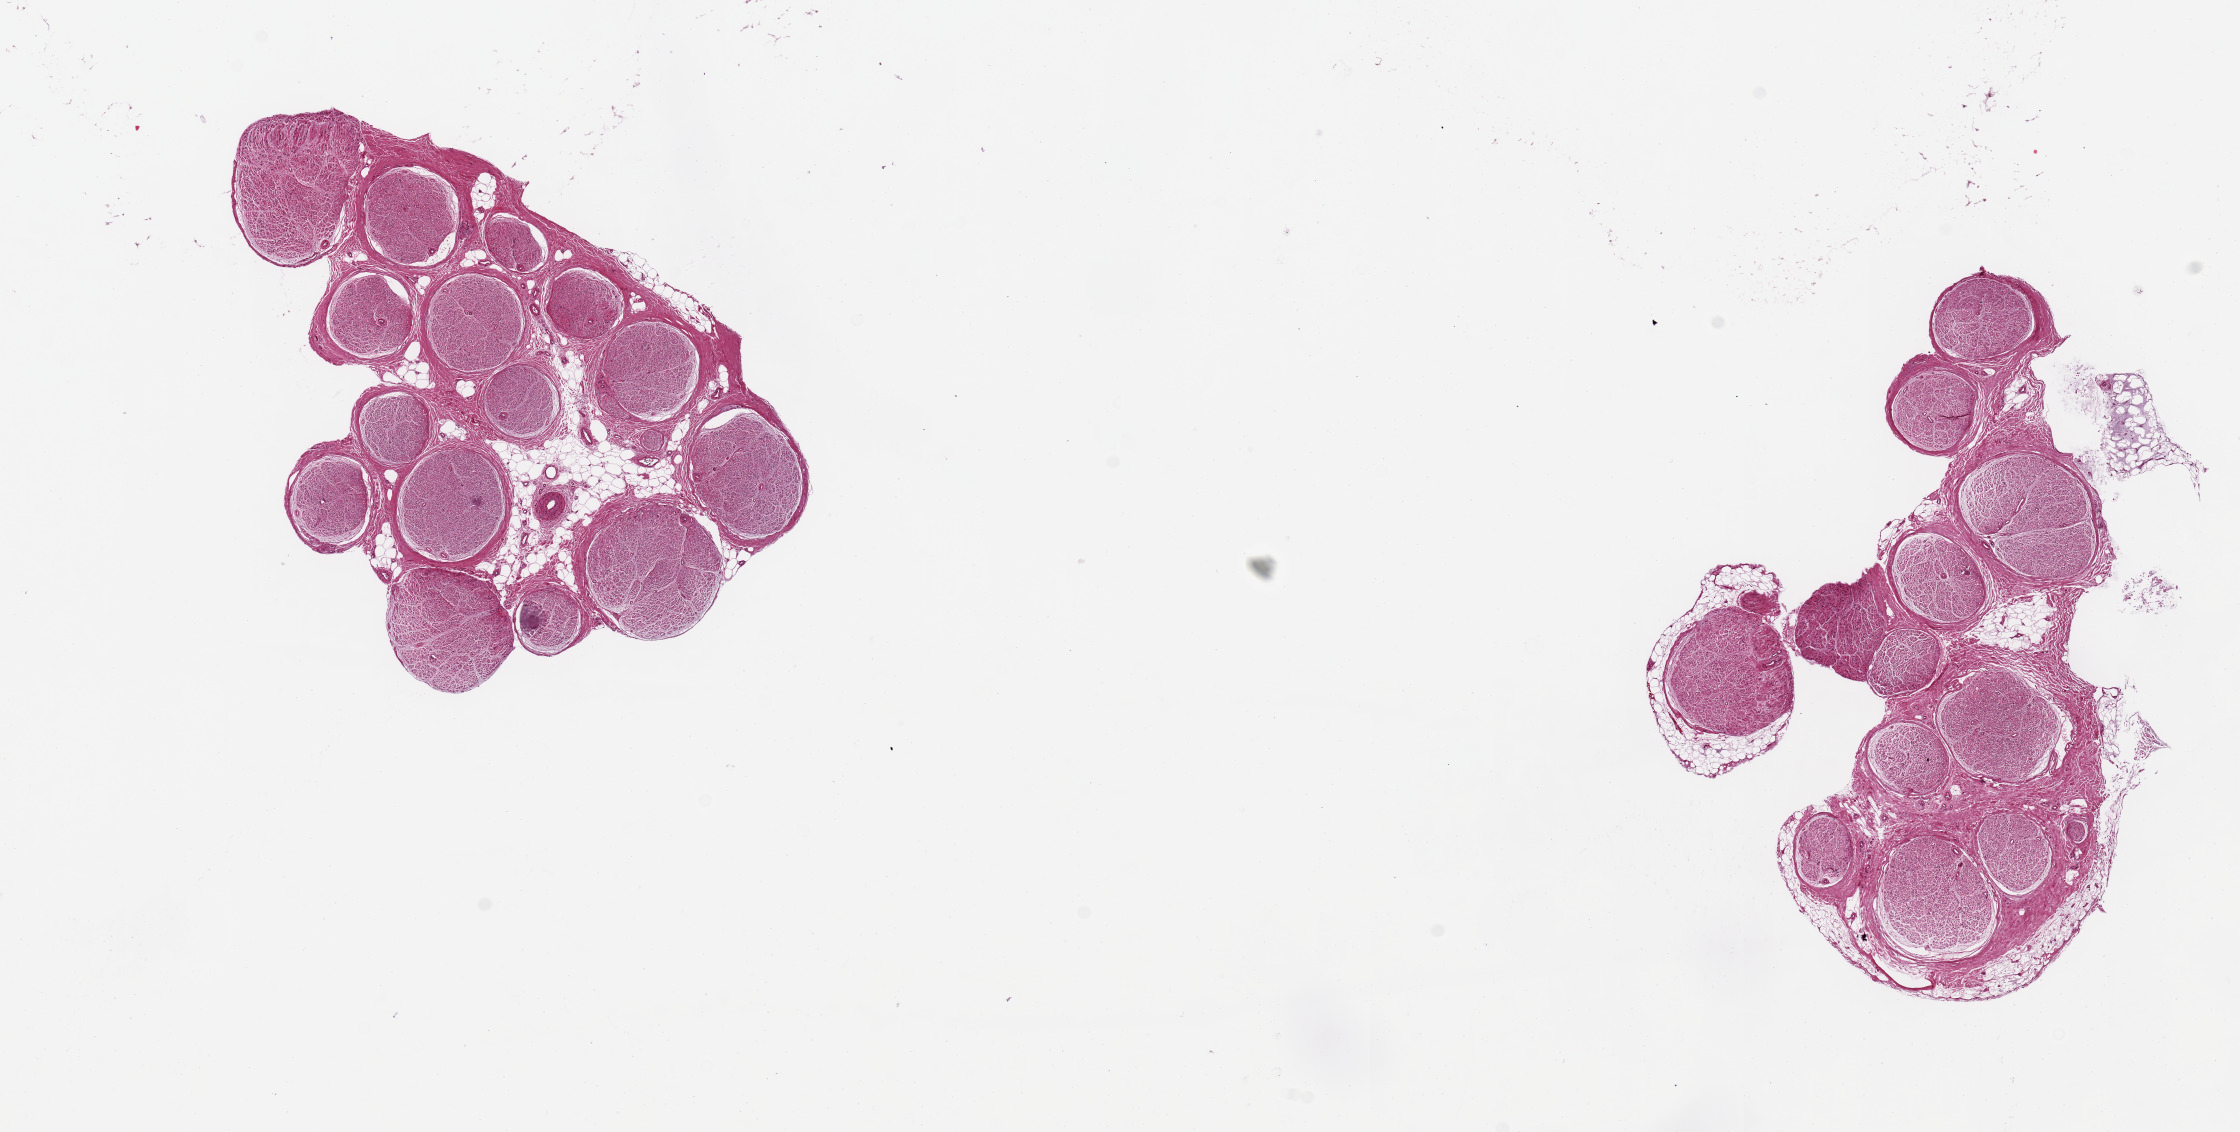
Haematoxylin and eosin whole-slide image — shown as a low-resolution overview of the whole scanned area (about 17.7 x 9.0 mm); PAXgene-fixed, paraffin-embedded tissue; sampled site (target tissue): tibial nerve; tissue donor sample. Donor sex: male.
Reviewer comment on this tissue sample: 2 pieces 5x4 & 6x4.5mm; good clean specimens.